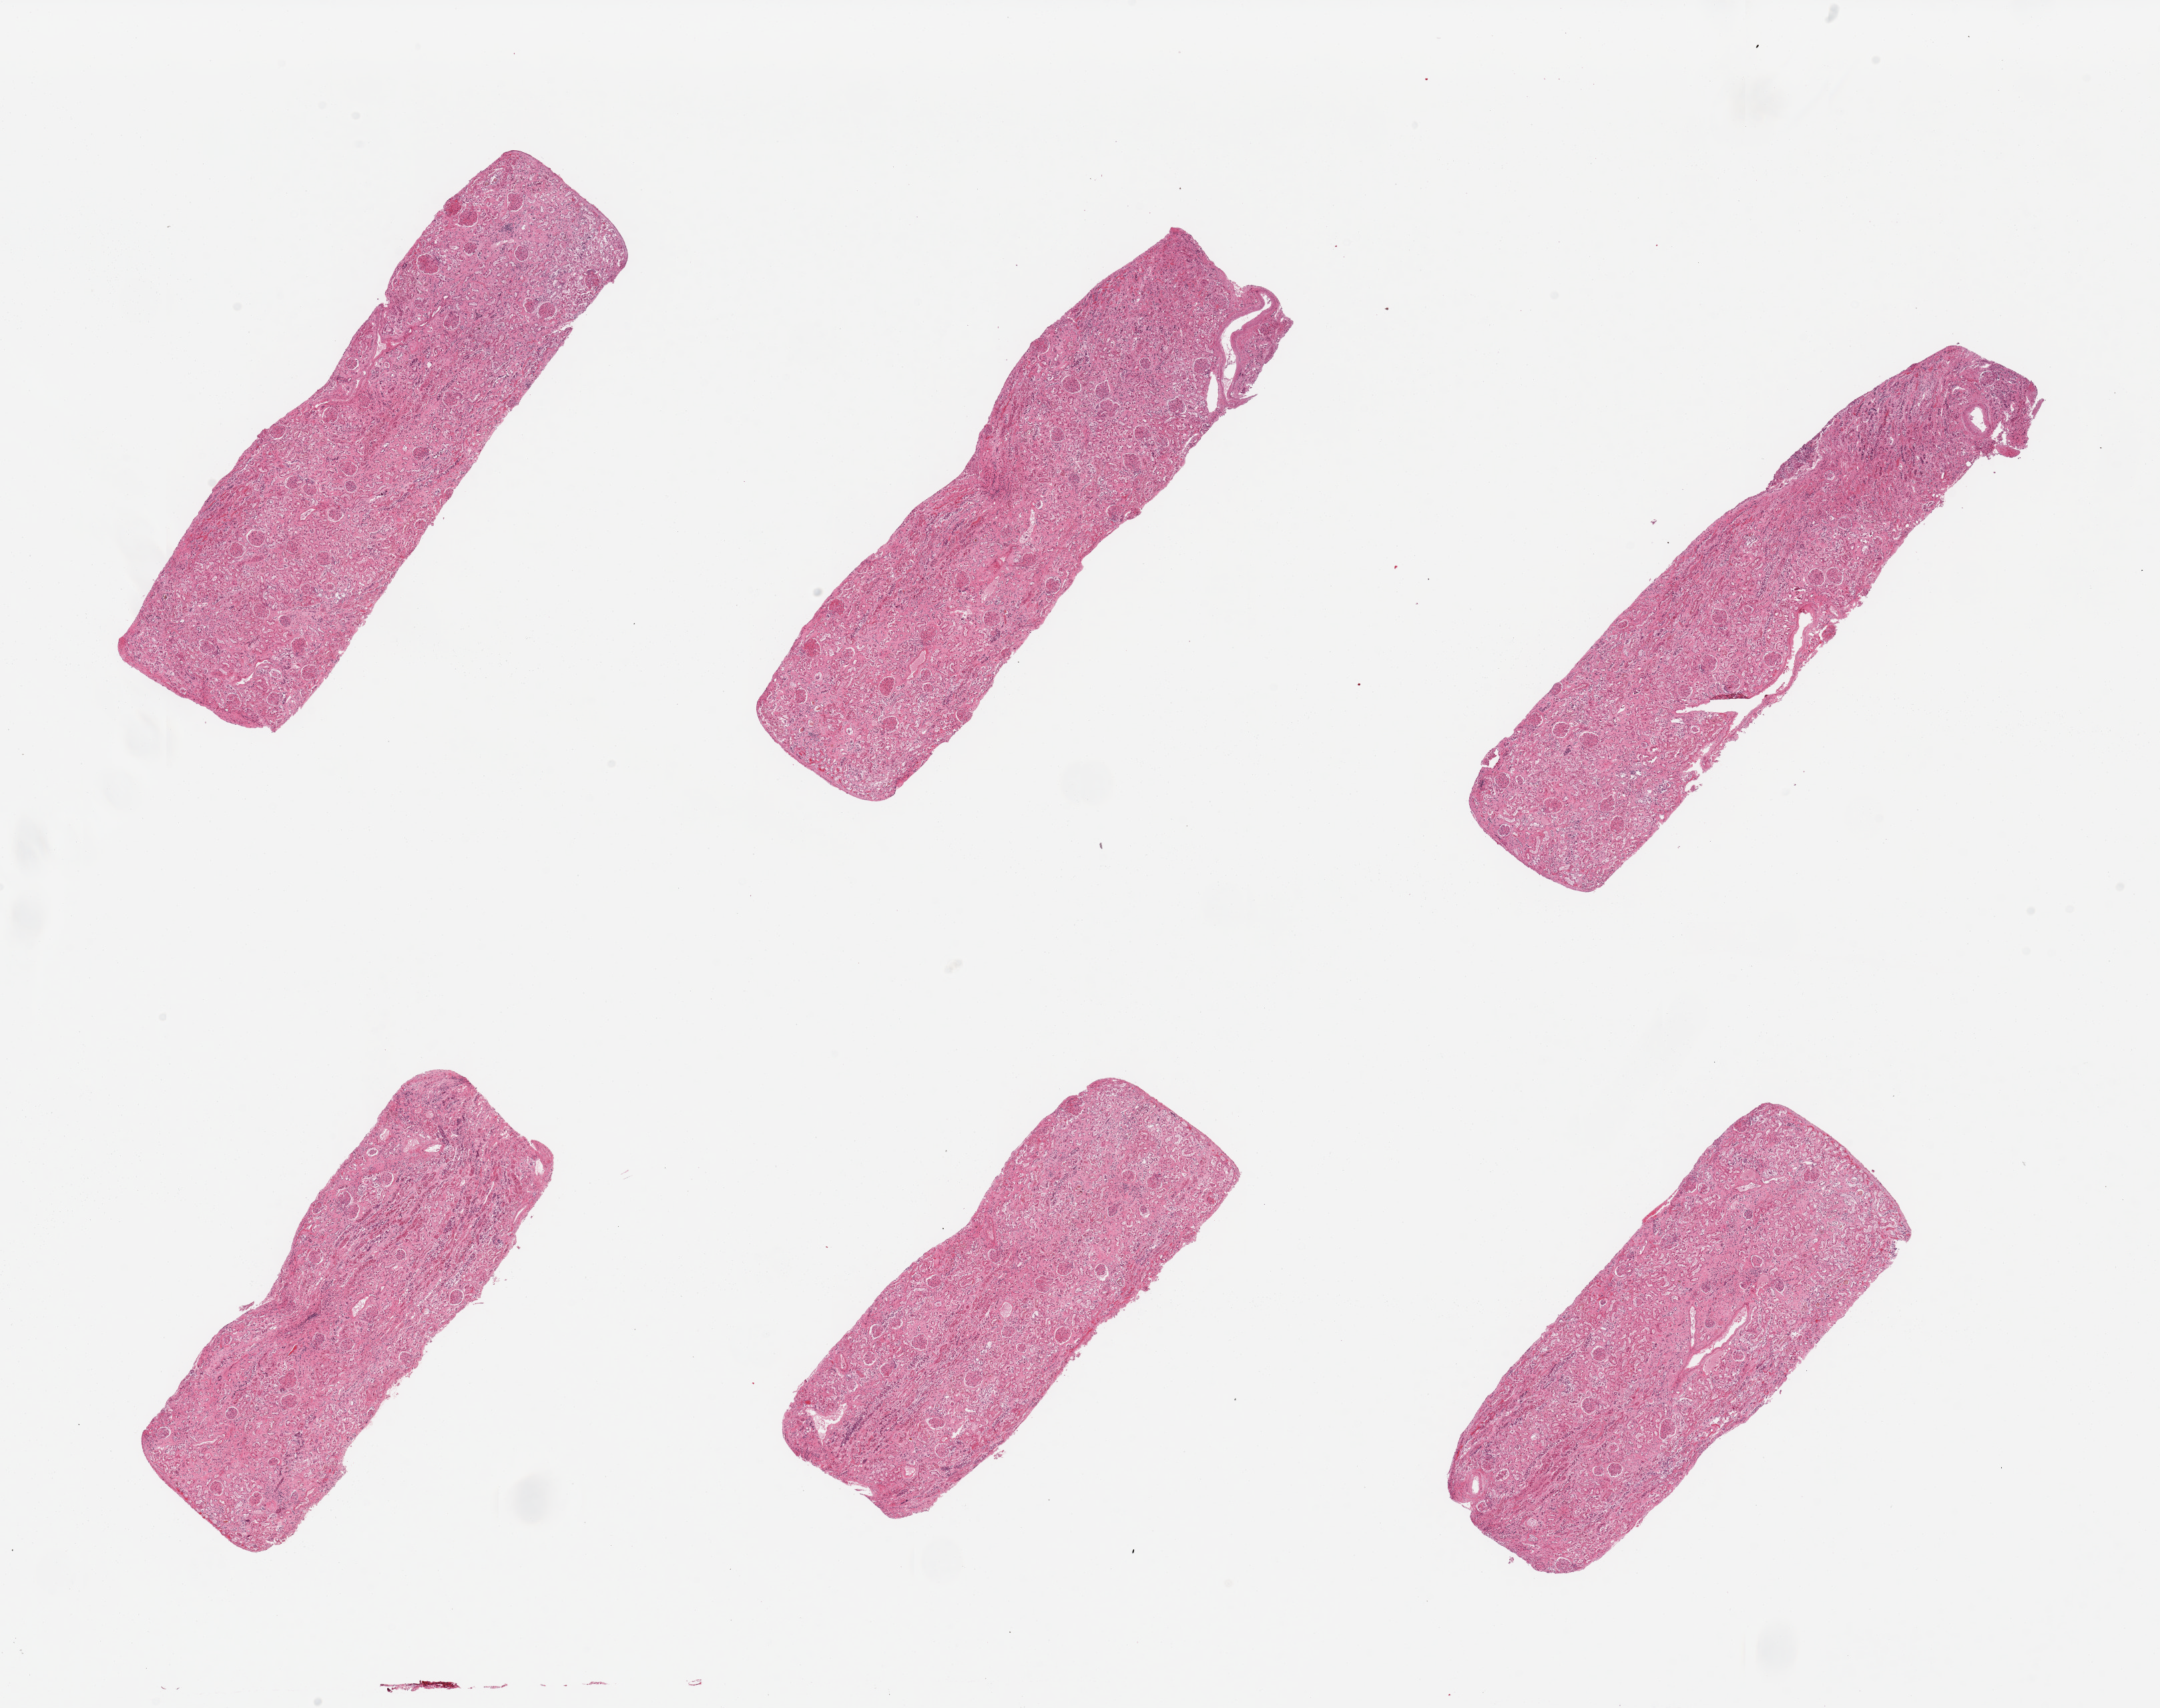
Hematoxylin and eosin (H&E) whole-slide image, brightfield, a low-resolution overview of the entire scanned area, about 25.6 x 20.2 mm (from a 20x scan). PAXgene-fixed paraffin-embedded (PFPE) section. Section of renal cortex (target tissue). Donor tissue sample. Male donor.
Pathologist's review note for this sample: 6 pieces; tubules & ducts severely autolyzed; glomeruli preserved; moderate interstitial fibrosis; no notable vascular lesions.